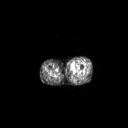
FDG PET of an extremity soft-tissue mass (from a PET/CT study), one axial slice; slice 231 of 267 in the series (ordered by position); 3.27 mm slice thickness; 128 × 128 image matrix. Patient: male, 48 years. From the clinical record (not read from this slice): histological type: pleiomorphic leiomyosarcoma; grade: high; site of the primary tumour: left thigh.
Outlined on this slice (expert contour drawn on MRI and transferred to this co-registered scan by the dataset authors):
- gross tumour volume including surrounding oedema: bounding box (x1, y1, x2, y2) in pixels: (70, 64, 75, 70)
- gross tumour volume (mass): (71, 67, 74, 70)